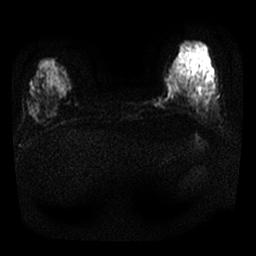
Breast MRI, one axial slice. Position 7 of 25 along the scan axis. Diffusion-weighted series; image 2 of 4 stored at this slice position (different b-values; order by instance number). 1.5 T. 4 mm slice thickness. 256 × 256 image matrix, field of view 300 × 300 mm. Female patient.
Annotated regions visible in this slice (outlined manually by an expert reader):
- tumour on diffusion-weighted imaging: bounding box [x1, y1, x2, y2] px = [154, 74, 175, 106]